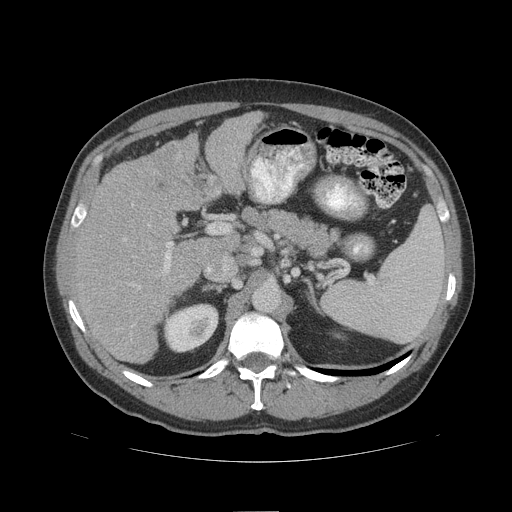
Contrast-enhanced abdominal CT (liver protocol), one axial slice; position 64 of 109 along the scan axis; reconstruction kernel STANDARD; 140 kVp; soft-tissue window (W 400 / L 40 HU); 2.5 mm slice thickness; 512 × 512 image matrix. Case-level facts recorded for this patient, not image findings: diagnosis: hepatocellular carcinoma (patient treated with transarterial chemoembolisation; whether this scan precedes or follows treatment is not stated here); TNM stage (as recorded): Stage-IIIB; Child-Pugh class: A; tumour nodularity: multinodular.
Outlined on this slice (semi-automatically segmented with operator editing):
- liver parenchyma outside the tumour (the mass and vessels are separate outlines, so this box may not span the whole liver): bounding box (x1, y1, x2, y2) in pixels: (72, 110, 264, 364)
- liver vessels: (164, 242, 173, 273)